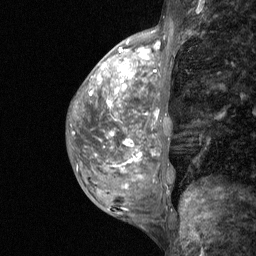
Breast MRI (dynamic contrast-enhanced), one sagittal slice. Slice 23 of 64 in the series (ordered by position). Dynamic contrast-enhanced study with each time point stored as its own series, time point 2 of 3 at this slice position (early post-contrast, ordered by acquisition time). 1.5 T. TE 4.8 ms, TR 27 ms. 2 mm slice thickness. 256 × 256 image matrix. Patient: female, 36 years. From the clinical record (not read from this slice): setting: breast cancer imaged before/during neoadjuvant chemotherapy; receptor status: HR-positive, HER2-negative.
Structures marked on this image (semi-automatic segmentation, software-assisted and operator-edited):
- analysis volume of interest (the breast-tissue region the enhancement analysis was run in; not a lesion): bounding box (x1, y1, x2, y2) in pixels: (73, 58, 174, 210)
- tumour enhancement mask (voxels above the 90 % enhancement threshold inside the analysis volume of interest): (116, 61, 129, 92)